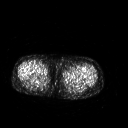
FDG PET of an extremity soft-tissue mass (from a PET/CT study), one axial slice. 3.27 mm slice thickness. 128 × 128 image matrix. Patient: female, 42 years. Case-level facts recorded for this patient, not image findings: histological type: pleiomorphic leiomyosarcoma; grade: intermediate; site of the primary tumour: left thigh.
Structures marked on this image (expert contour drawn on MRI and transferred to this co-registered scan by the dataset authors):
- gross tumour volume including surrounding oedema: box from (x=64, y=71) to (x=81, y=80) px